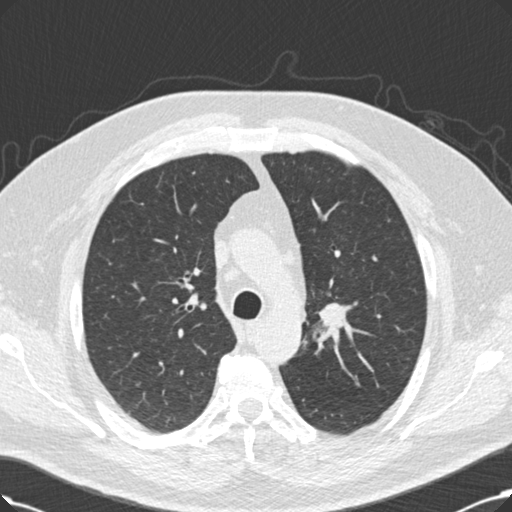
Low-dose screening chest CT, axial slice. Third annual screen. Lung window (W 1500 / L -600 HU). 2 mm slice thickness. Standard (soft-tissue) reconstruction kernel (B30f). Male, age 60 years at enrolment. Current smoker at enrolment.
Lesion marked by an expert reader, bounding box <318,298,349,332> (left, top, right, bottom; pixels). Screening reader's record for this exam (one nodule recorded; not confirmed to be the boxed lesion): non-calcified nodule or mass ≥4 mm, left upper lobe, 20 × 20 mm, smooth margins, soft tissue attenuation, pre-existing on the prior screen: no. Participant outcome: lung cancer diagnosed 53 days after this screen — squamous cell carcinoma, NOS, right upper lobe, 27 mm at pathology.